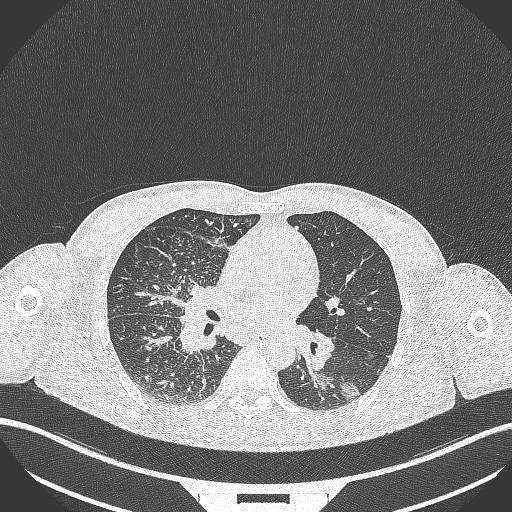
Chest CT, one axial slice. 120 kVp. Lung window (W 1500 / L -600 HU). 512 × 512 image matrix. Patient: male, 49 years. Case-level facts recorded for this patient, not image findings: clinical TNM (as recorded): T2b N1 M0.
Outlined on this slice (bounding box drawn by a radiologist):
- lung tumour (recorded histology: adenocarcinoma): bounding box <311,367,365,402> (left, top, right, bottom; pixels)